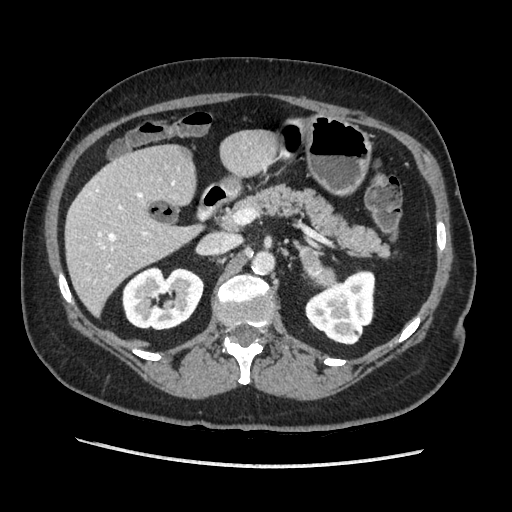
Contrast-enhanced abdominal CT, one axial slice. Slice 111 of 203 in the series (ordered by position). Soft-tissue window (W 400 / L 40 HU). 1.25 mm slice thickness. 512 × 512 image matrix, field of view 360 × 360 mm. Female patient. Case-level facts recorded for this patient, not image findings: diagnosis: adrenocortical carcinoma; tumour side: left adrenal; tumour size at pathology: 6.5 cm; Ki-67 index: 22 %; stage (as recorded): 2.
Outlined on this slice (semi-automatic segmentation, software-assisted and operator-edited):
- mass: bounding box <300,248,335,284> (left, top, right, bottom; pixels)